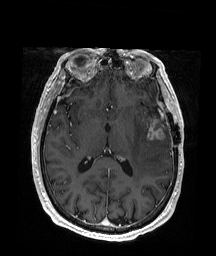
Brain MRI from a brain-tumour surgery series, one axial slice. Position 93 of 176 along the scan axis. T1-weighted post-contrast. 1 mm slice thickness. 216 × 256 image matrix, field of view 219 × 260 mm. Case-level facts recorded for this patient, not image findings: histopathology: Glioblastoma; WHO grade: 4; IDH mutation: no.
Structures marked on this image (manually delineated by an expert):
- tumour: bounding box [x1, y1, x2, y2] px = [147, 116, 166, 140]